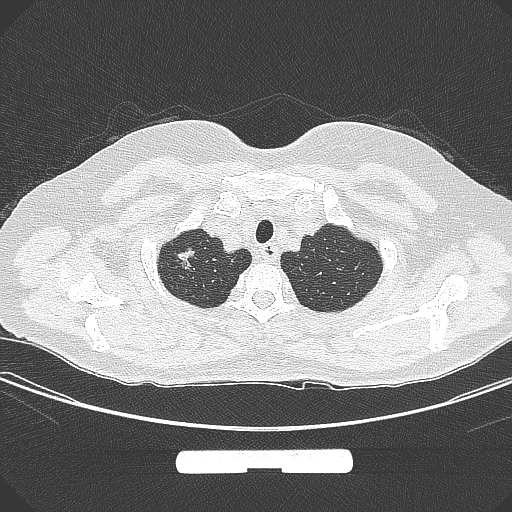
Chest CT, one axial slice. Position 263 of 295 along the scan axis. 120 kVp. Lung window (W 1500 / L -600 HU). 512 × 512 image matrix, field of view 369 × 369 mm. Female patient, age 58 years. From the clinical record (not read from this slice): clinical TNM (as recorded): T1b N0 M0; histopathological grade: G2-3.
Annotated regions visible in this slice (bounding box drawn by a radiologist):
- lung tumour (recorded histology: adenocarcinoma): bounding box <172,245,207,277> (left, top, right, bottom; pixels)